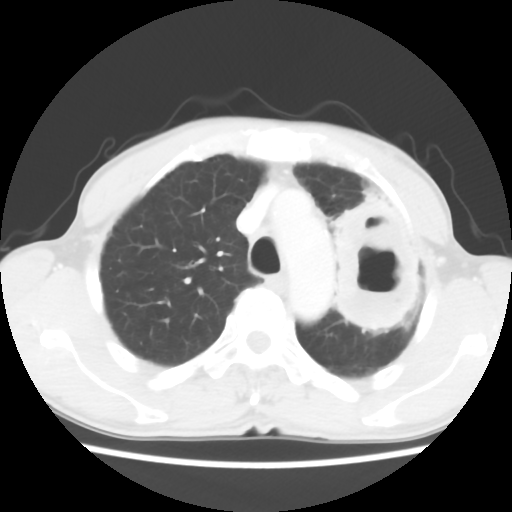
Chest CT, one axial slice; reconstruction kernel STANDARD; 120 kVp; lung window (W 1500 / L -600 HU); 5 mm slice thickness; 512 × 512 image matrix. Male patient, age 64 years. Case-level facts recorded for this patient, not image findings: clinical TNM (as recorded): T3 N3 M0; histopathological grade: G3.
Outlined on this slice (rectangle marked by the reading radiologist):
- lung tumour (recorded histology: adenocarcinoma): bounding box [x1, y1, x2, y2] px = [315, 183, 428, 341]